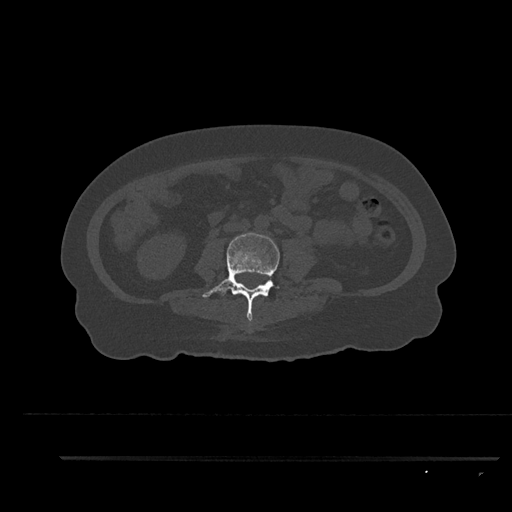
CT including the spine, one axial slice. Slice 83 of 797 in the series (ordered by position). Reconstruction kernel Br40s/3. Bone window (W 1800 / L 400 HU). 0.5 mm slice thickness. 512 × 512 image matrix, field of view 408 × 408 mm. Female patient, age 44 years. Case-level facts recorded for this patient, not image findings: primary cancer: renal; vertebrae with lytic lesions (as recorded): L1.
Annotated regions visible in this slice (semi-automatic segmentation, software-assisted and operator-edited):
- L3 vertebra: bounding box (x1, y1, x2, y2) in pixels: (202, 232, 280, 322)